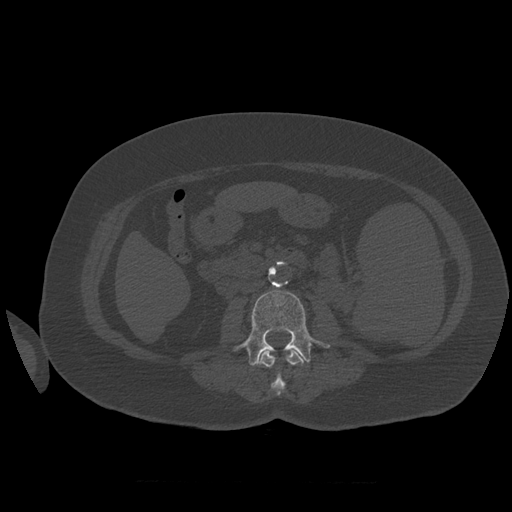
CT including the spine, one axial slice; slice 236 of 399 in the series (ordered by position); 120 kVp; bone window (W 1800 / L 400 HU); 1.25 mm slice thickness; 512 × 512 image matrix, field of view 404 × 404 mm. Patient age 81 years. Case-level facts recorded for this patient, not image findings: primary cancer: renal.
Annotated regions visible in this slice (semi-automatic segmentation, software-assisted and operator-edited):
- L2 vertebra: bounding box <258,350,307,395> (left, top, right, bottom; pixels)
- L3 vertebra: <234,291,330,367>